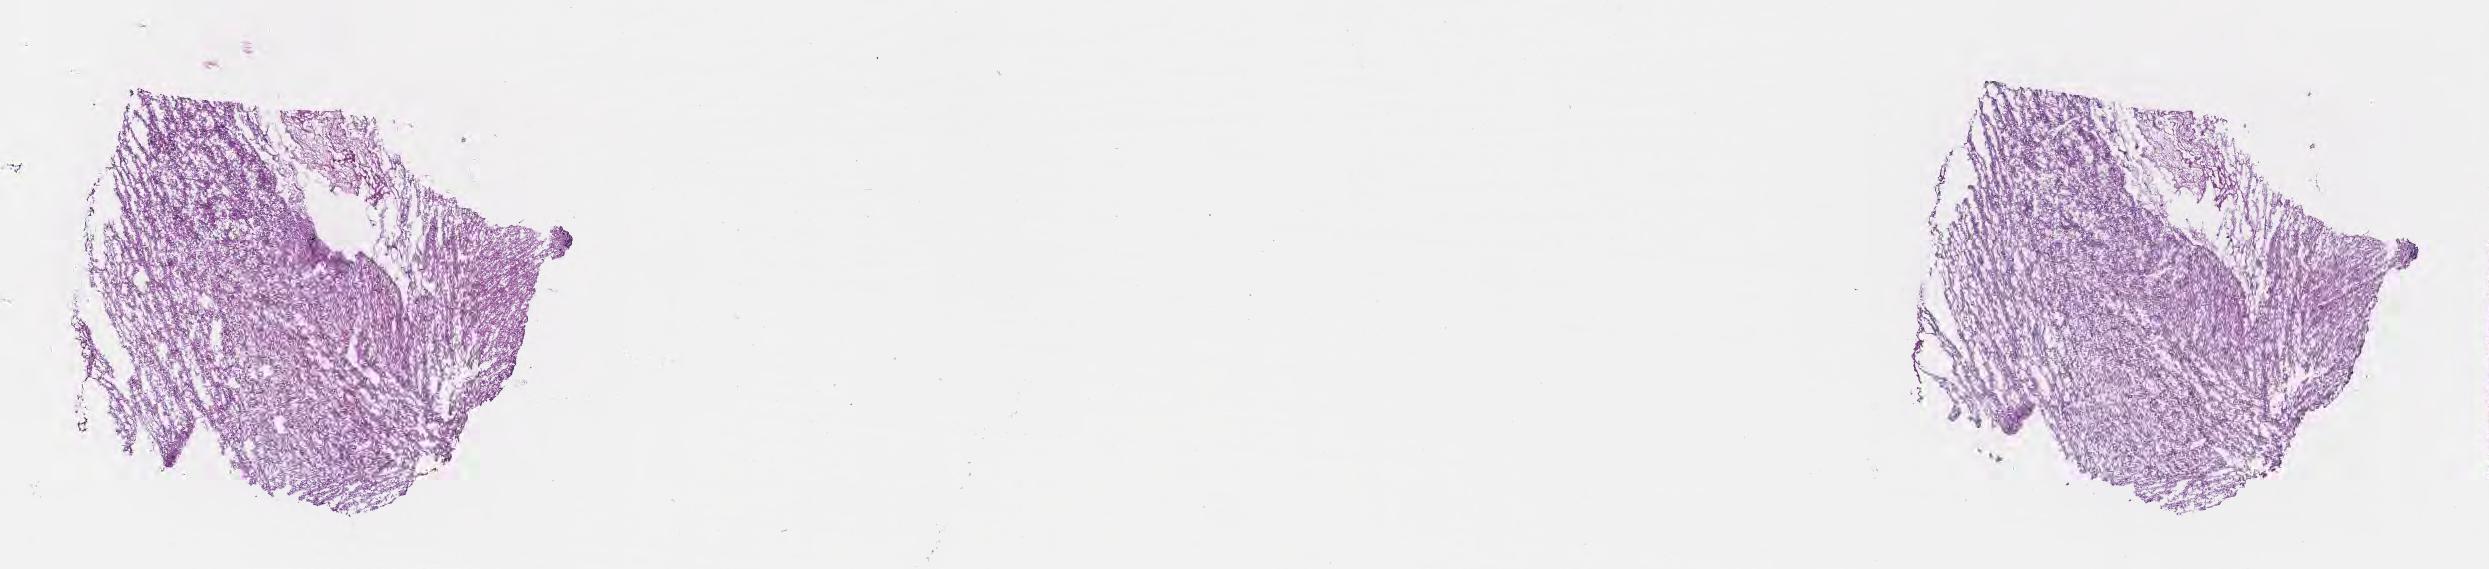
Whole-slide image, H&E stain — whole scanned area (about 20.1 x 4.6 mm) shown as a low-resolution overview; frozen section; recurrent tumor; site: brain. Female patient; age at initial diagnosis 58 years. Slide review estimates, as recorded: tumor cells 91%, tumor nuclei 98%, stromal cells 2%, necrosis 5%, normal cells 2%. Infiltration values recorded for this section: lymphocyte infiltration 0%, monocyte infiltration 0%, neutrophil infiltration 0%.
Patient diagnosis: Glioblastoma, NOS.